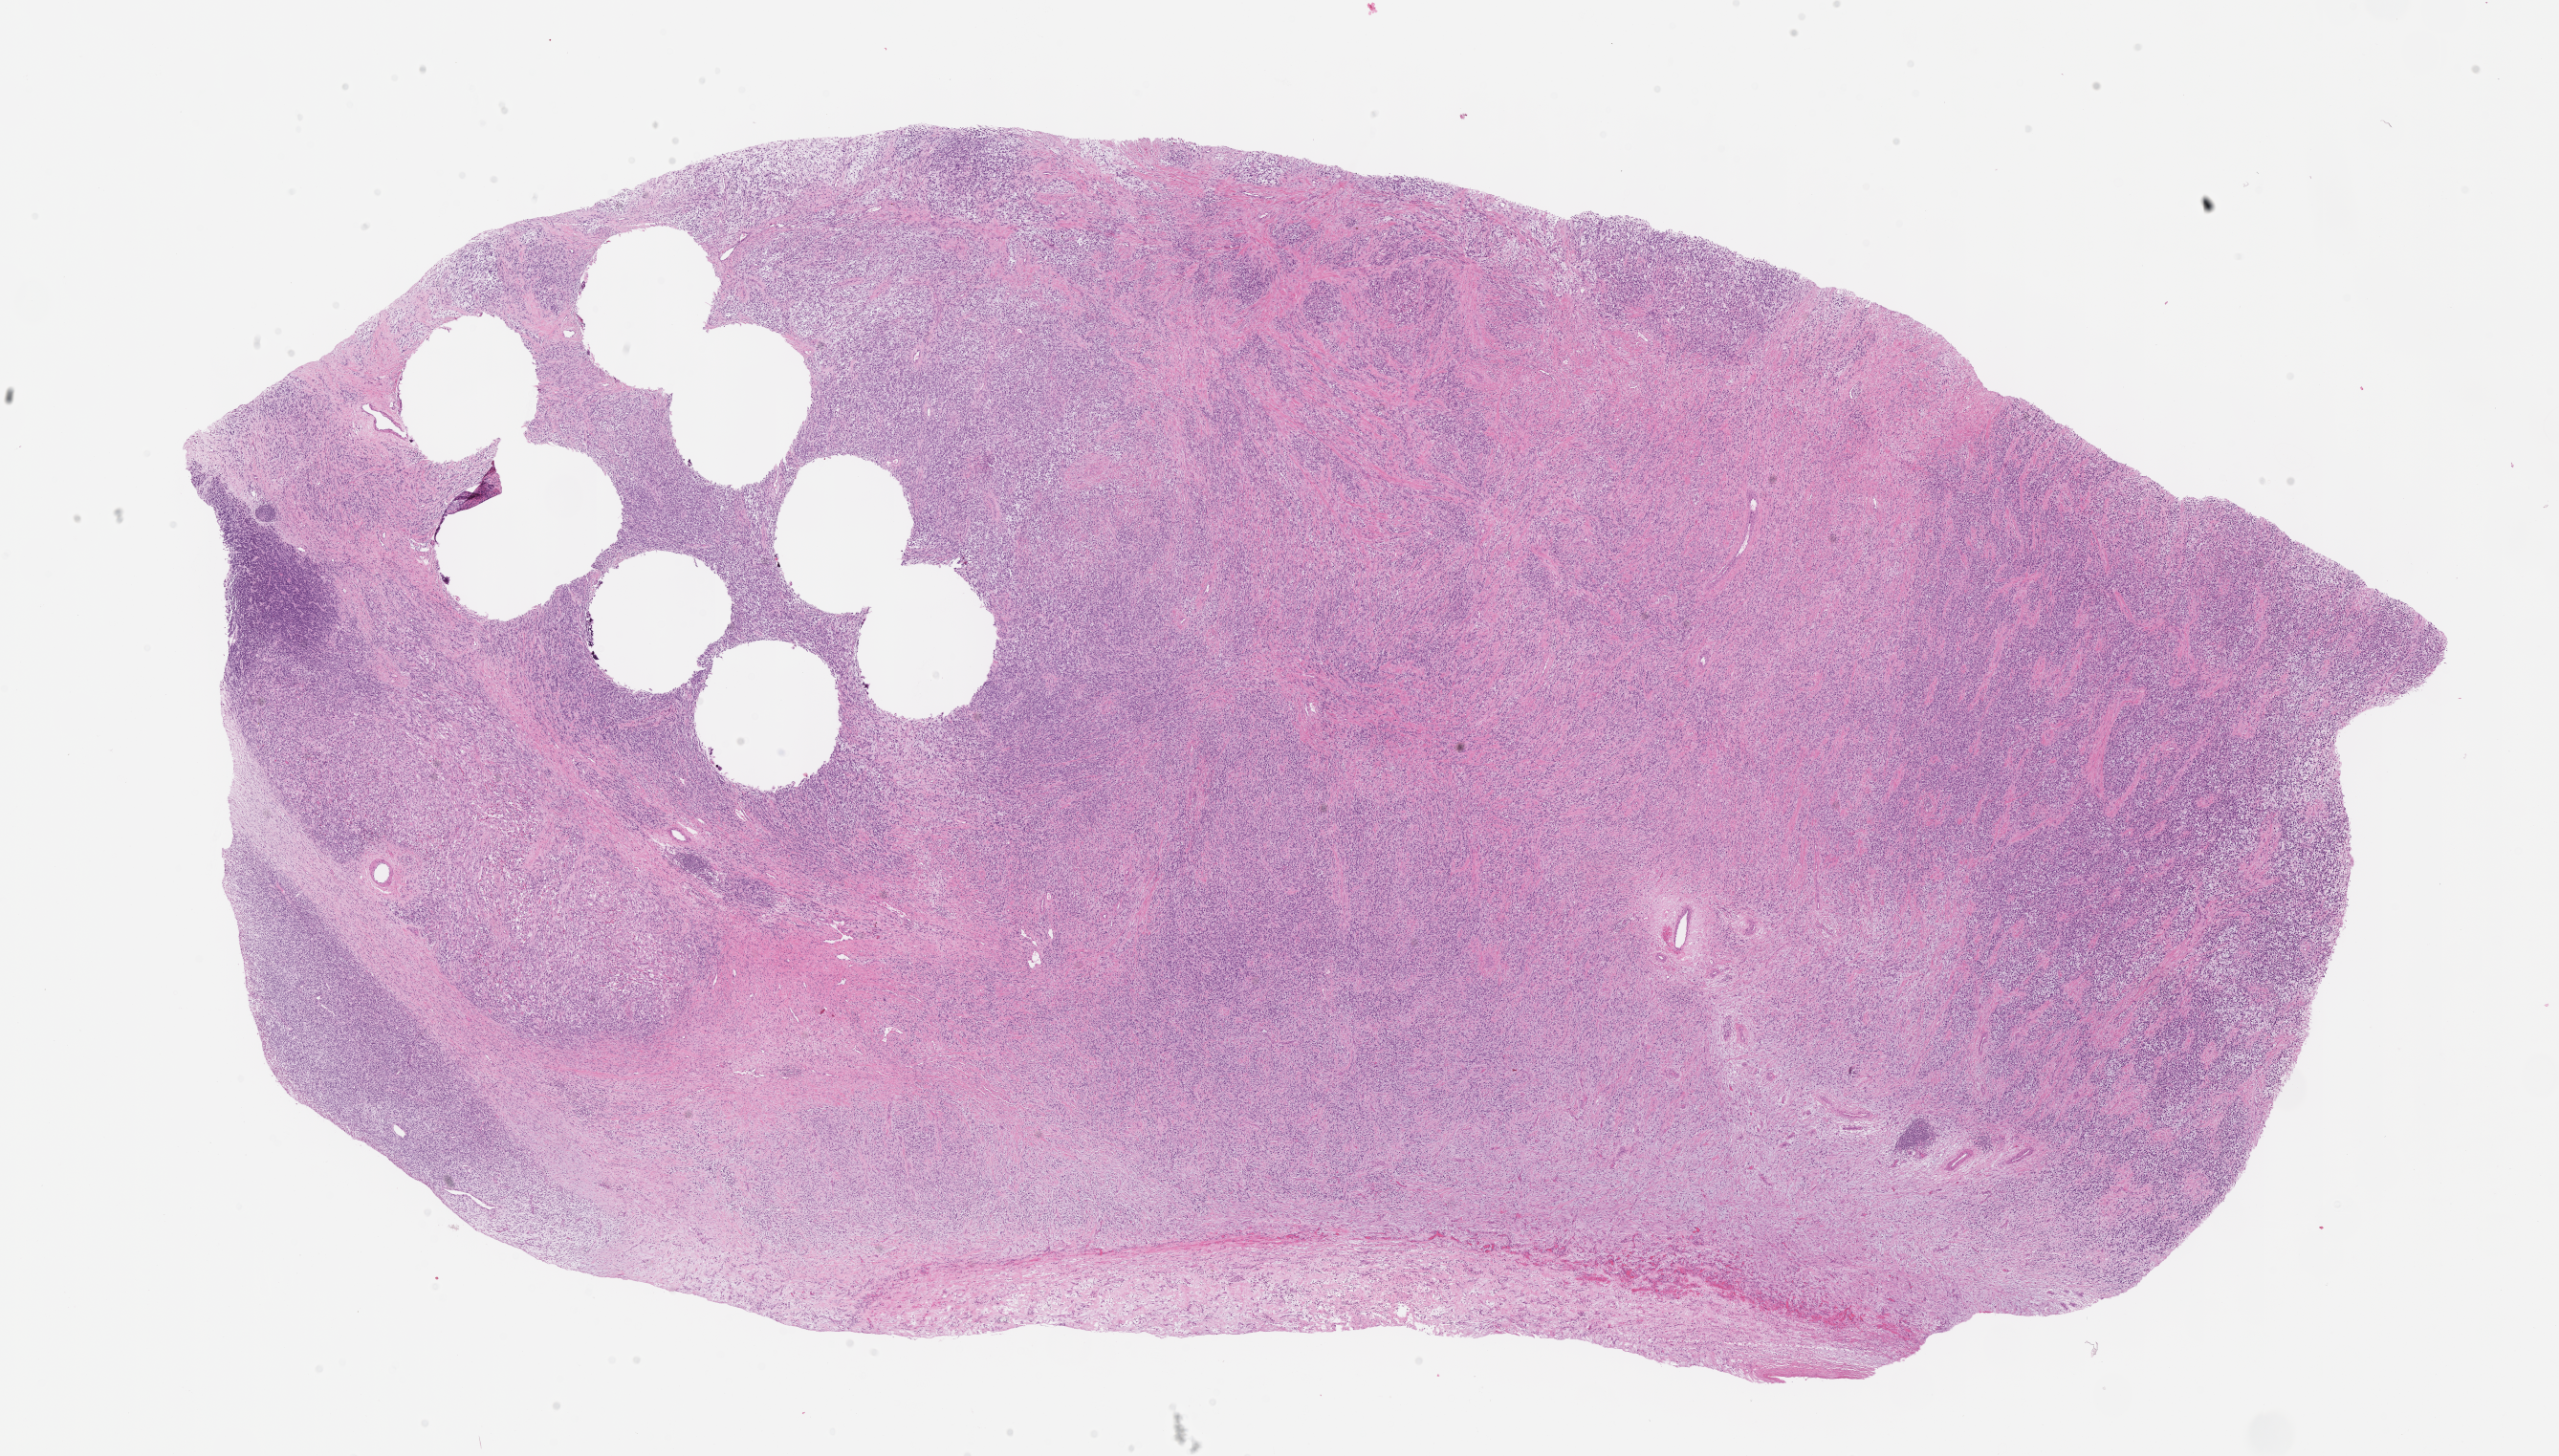
Digitized H&E-stained section of tumor tissue, a low-resolution overview of the entire scanned area, about 21.6 x 12.3 mm, formalin-fixed paraffin-embedded section, sample anatomic site: testis, right. Patient: male, age 6.1 years at diagnosis.
* diagnosis: rhabdomyosarcoma; histological classification: embryonal rhabdomyosarcoma
* stage (as recorded): 1
* metastatic status at presentation (as recorded): non-metastatic